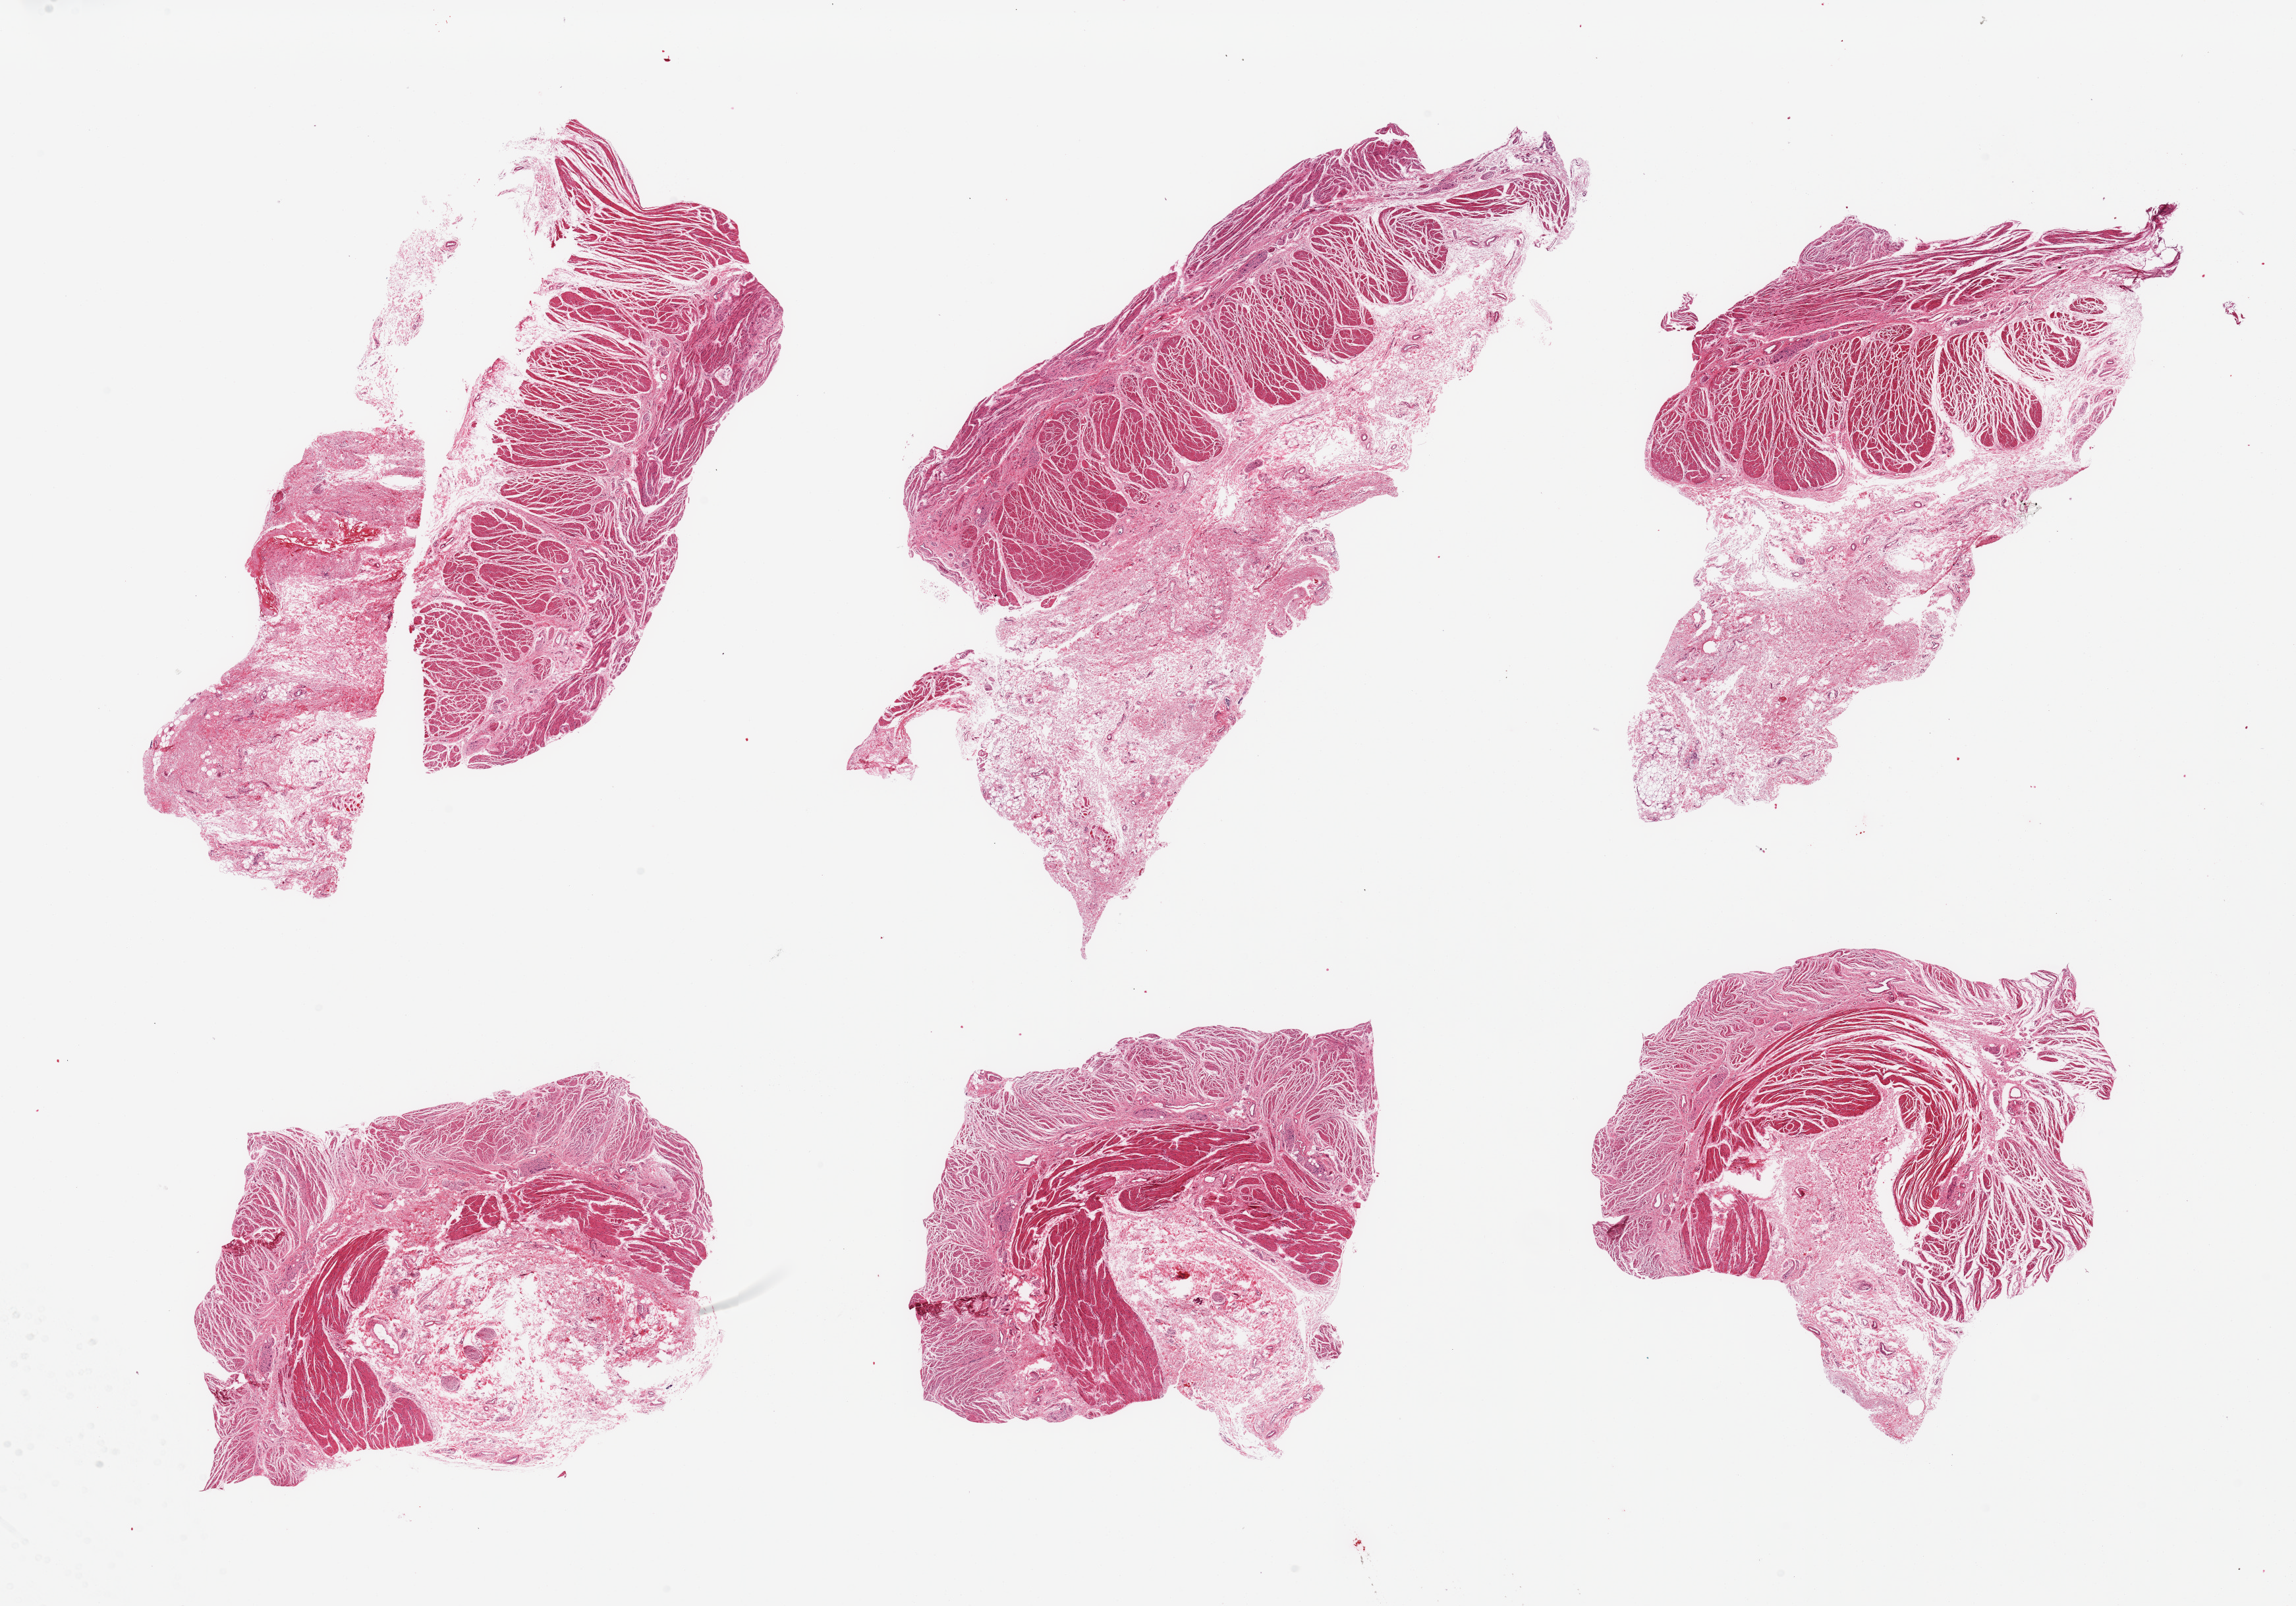
Digitized hematoxylin and eosin (H&E)-stained section, shown as a low-resolution overview of the whole scanned area (about 27.6 x 19.3 mm, acquisition: 20x scan), PAXgene-fixed paraffin-embedded (PFPE) section, target tissue: gastroesophageal junction, tissue donor sample.
* review note (as recorded): 6 pieces, confirmed target muscularis; adherent serosal fat up to ~4mm nubbins